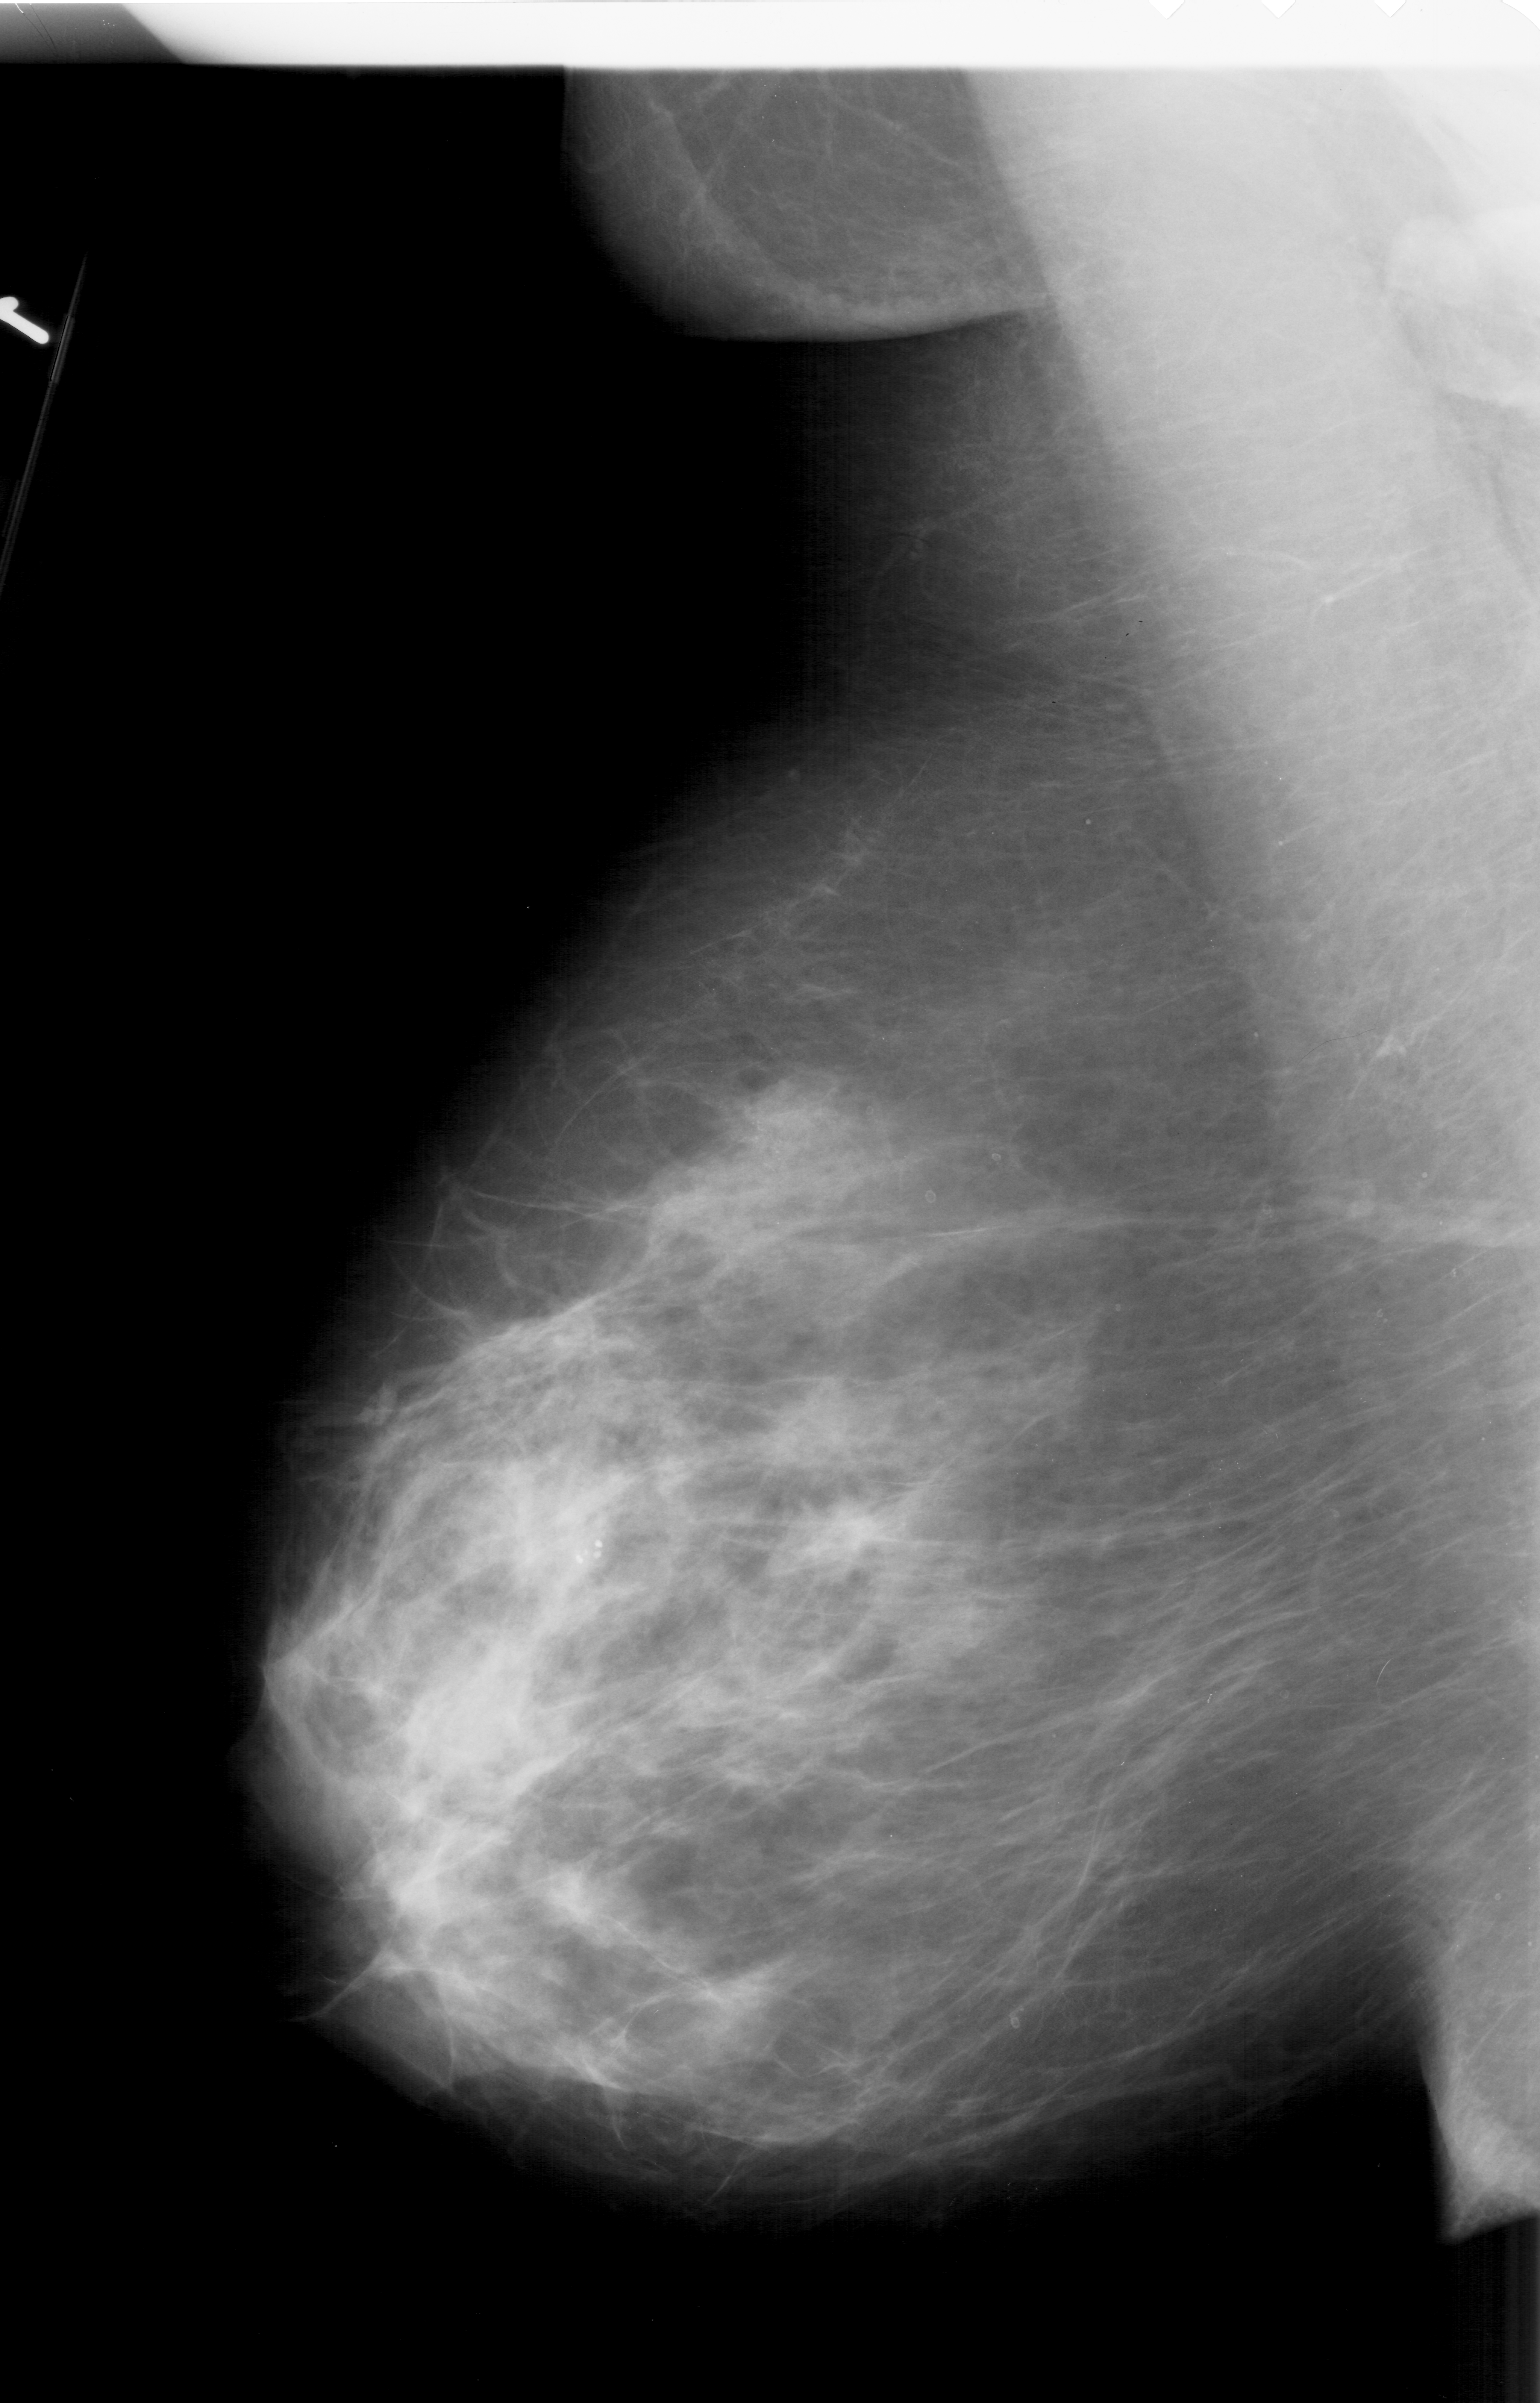
Scanned film-screen mammogram; left breast; mediolateral oblique (MLO) view; BI-RADS breast density category 4 (scale 1–4).
Calcifications, morphology pleomorphic, distribution clustered; BI-RADS assessment category 4; pathology result (as recorded, not read from the image): malignant.